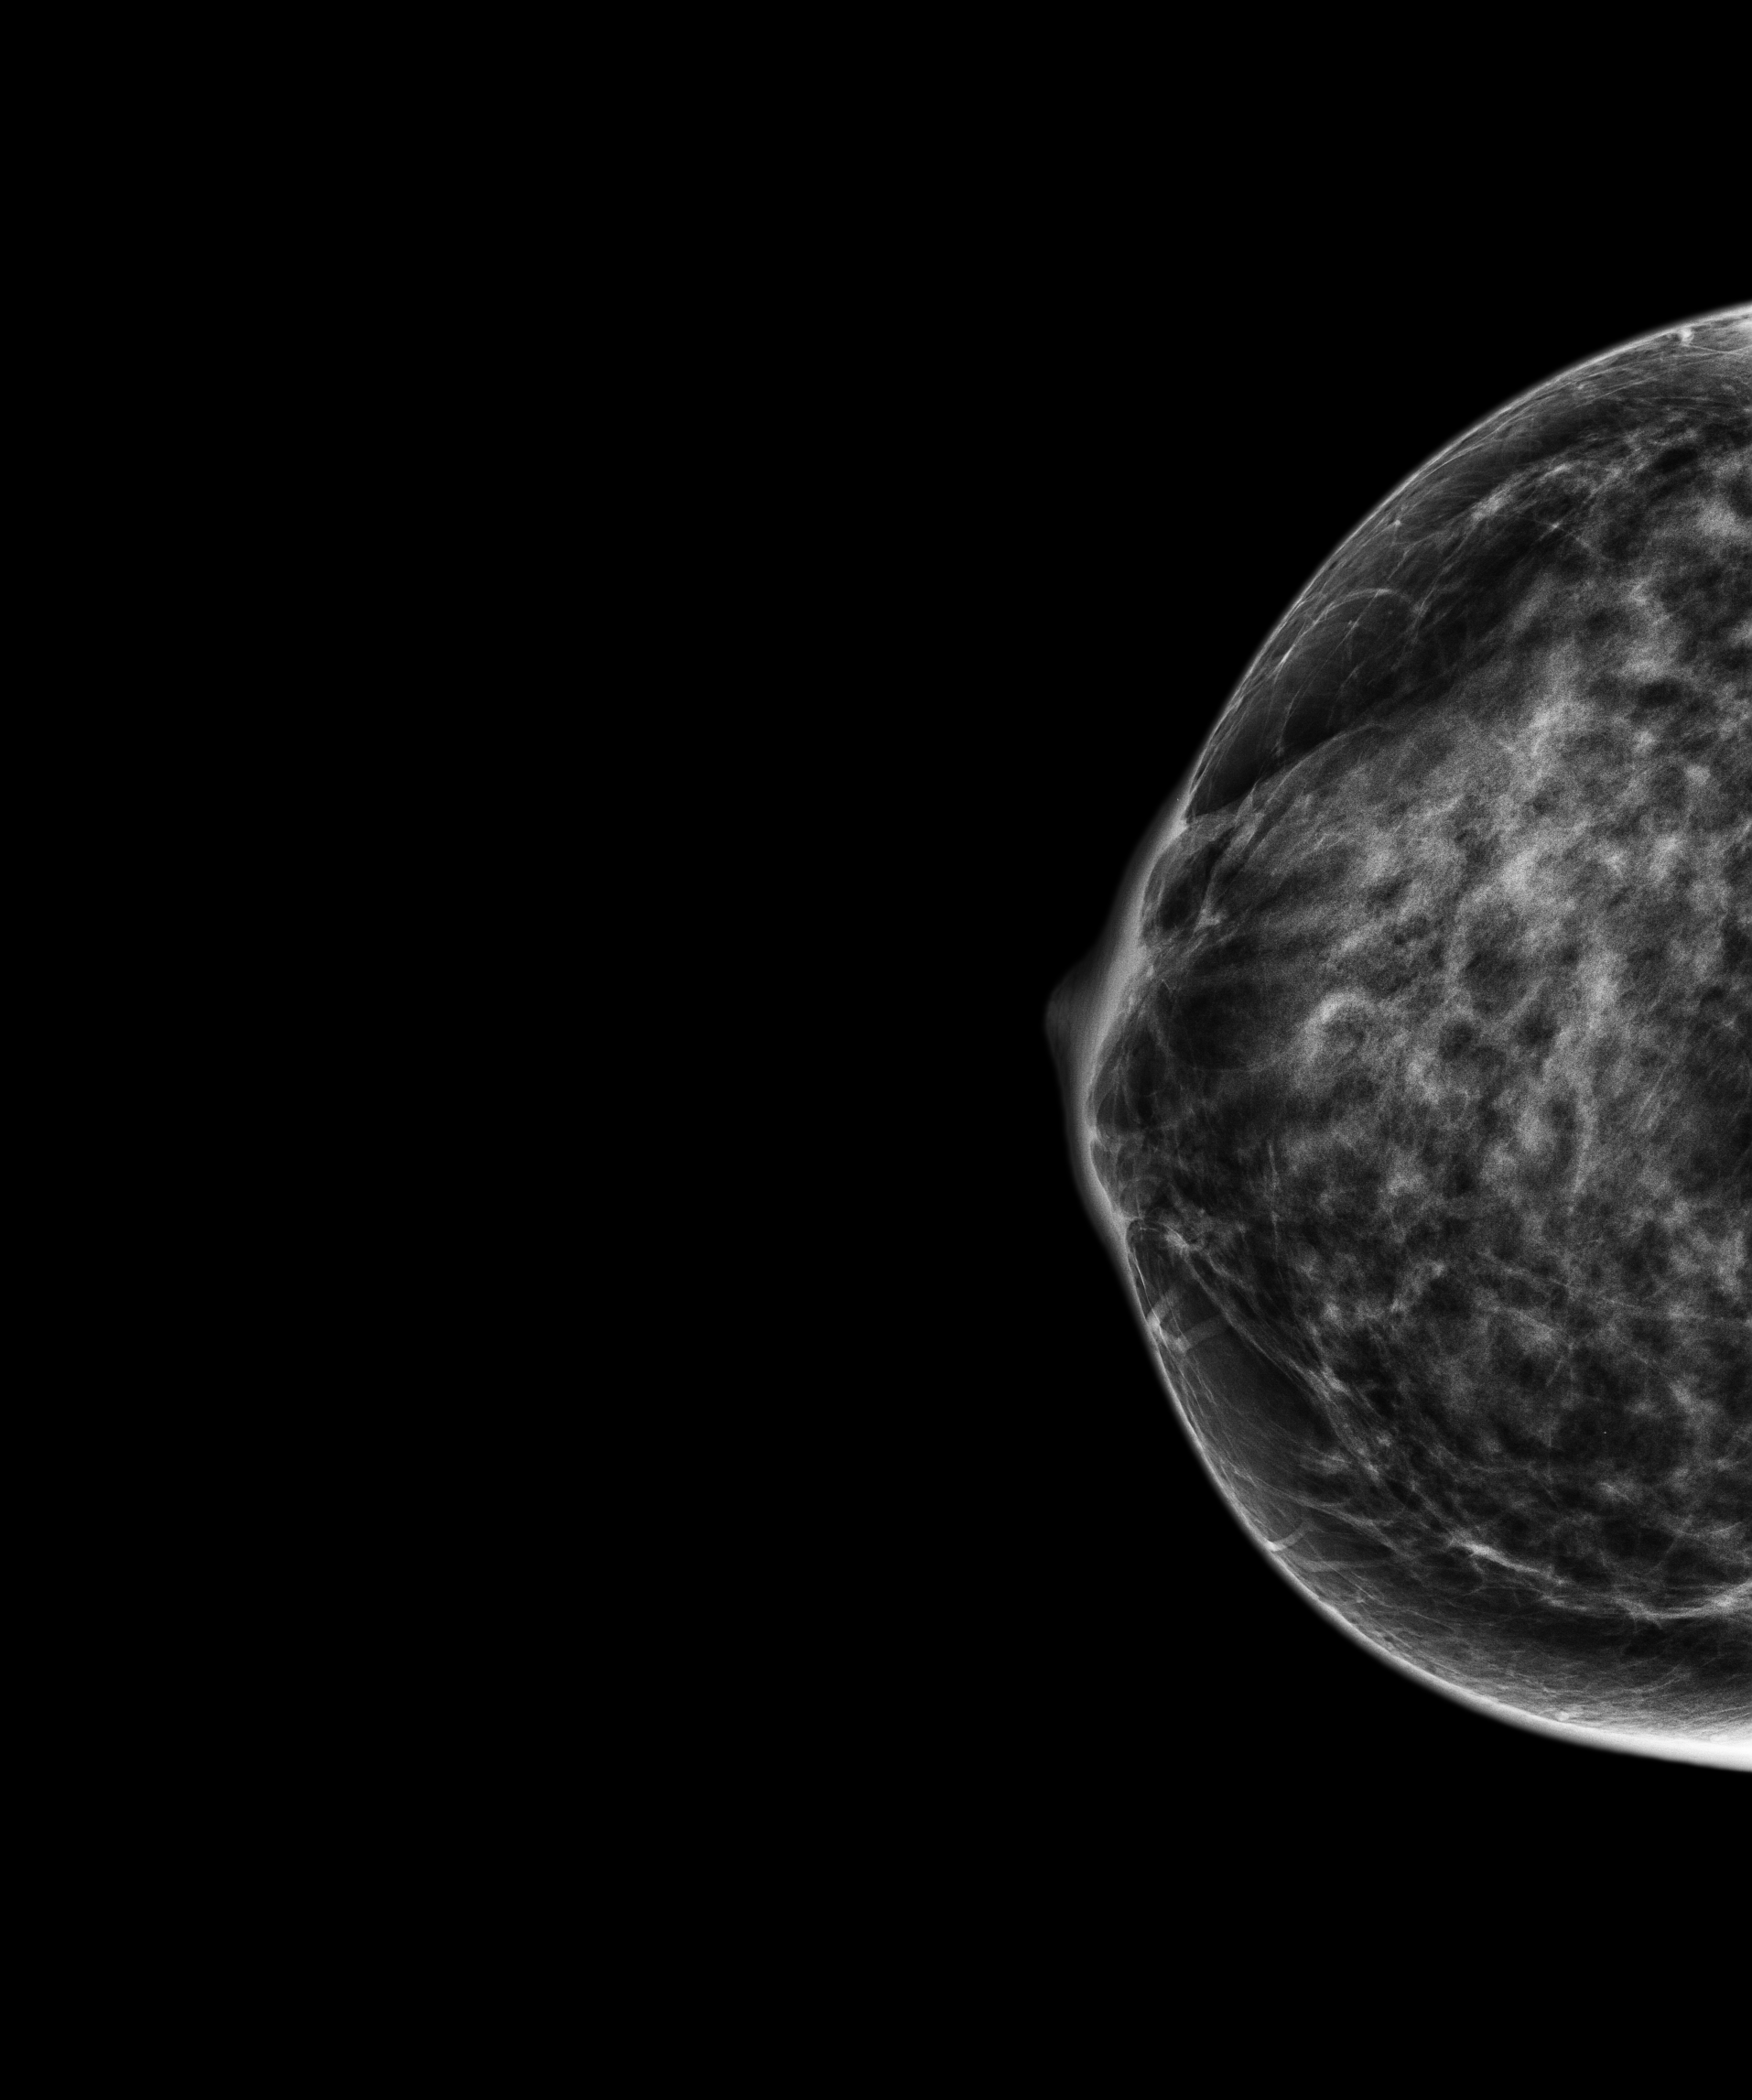
Screening examination. Patient aged 43 years (female).
Image type: full-field digital mammogram. Breast: right. Projection: craniocaudal (CC) view.